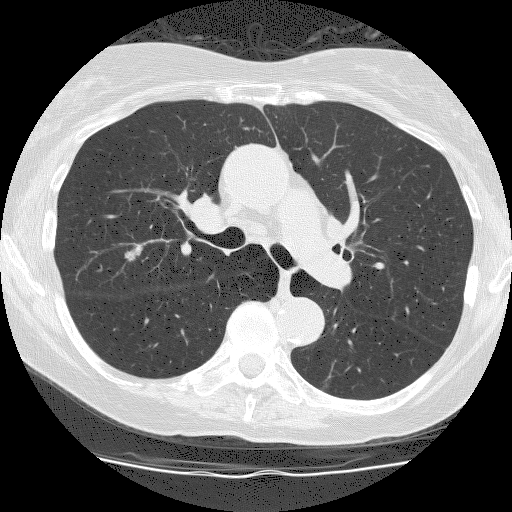
Chest CT (low-dose screening protocol), one axial image, second screening round (one year after baseline), lung window (W 1500 / L -600 HU), 2.5 mm slice thickness, slice 68 of 186 in the series. Female participant, aged 66 years at enrolment.
Expert reader's lesion annotation, bounding box <109,232,160,277> (left, top, right, bottom; pixels). The screening reader recorded 2 non-calcified nodules or masses ≥4 mm on this exam (right upper lobe, right lower lobe); which of them this box marks is not recorded.